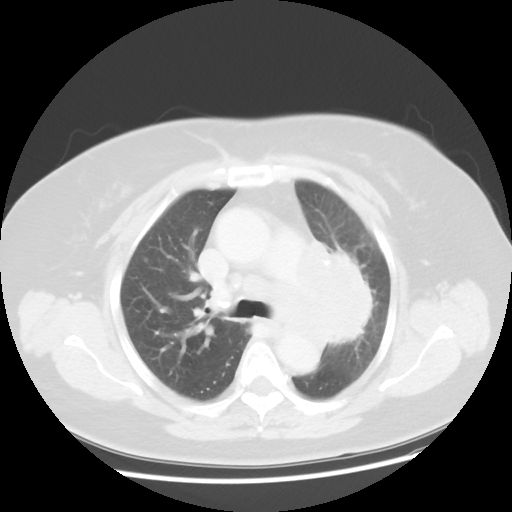
Chest CT, one axial slice; position 31 of 49 along the scan axis; reconstruction kernel STANDARD; 120 kVp; lung window (W 1500 / L -600 HU); 5 mm slice thickness; 512 × 512 image matrix, field of view 374 × 374 mm. Female patient, age 58 years. From the clinical record (not read from this slice): clinical TNM (as recorded): T4 N3 M0; histopathological grade: G3.
Structures marked on this image (bounding box drawn by a radiologist):
- lung tumour (recorded histology: small cell carcinoma): bounding box <272,236,375,355> (left, top, right, bottom; pixels)